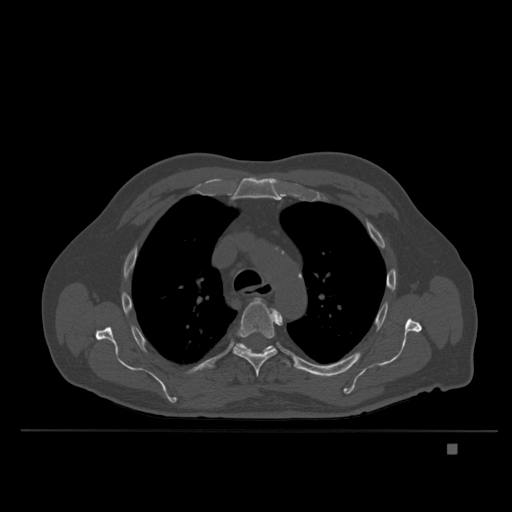
CT including the spine, one axial slice; position 272 of 435 along the scan axis; bone window (W 1800 / L 400 HU); 512 × 512 image matrix, field of view 434 × 434 mm. Patient: male, 73 years. Case-level facts recorded for this patient, not image findings: primary cancer: skin.
Structures marked on this image (semi-automatically segmented with operator editing):
- T3 vertebra: bounding box [x1, y1, x2, y2] px = [268, 346, 272, 349]
- T5 vertebra: [233, 298, 283, 377]
- T6 vertebra: [239, 345, 291, 367]